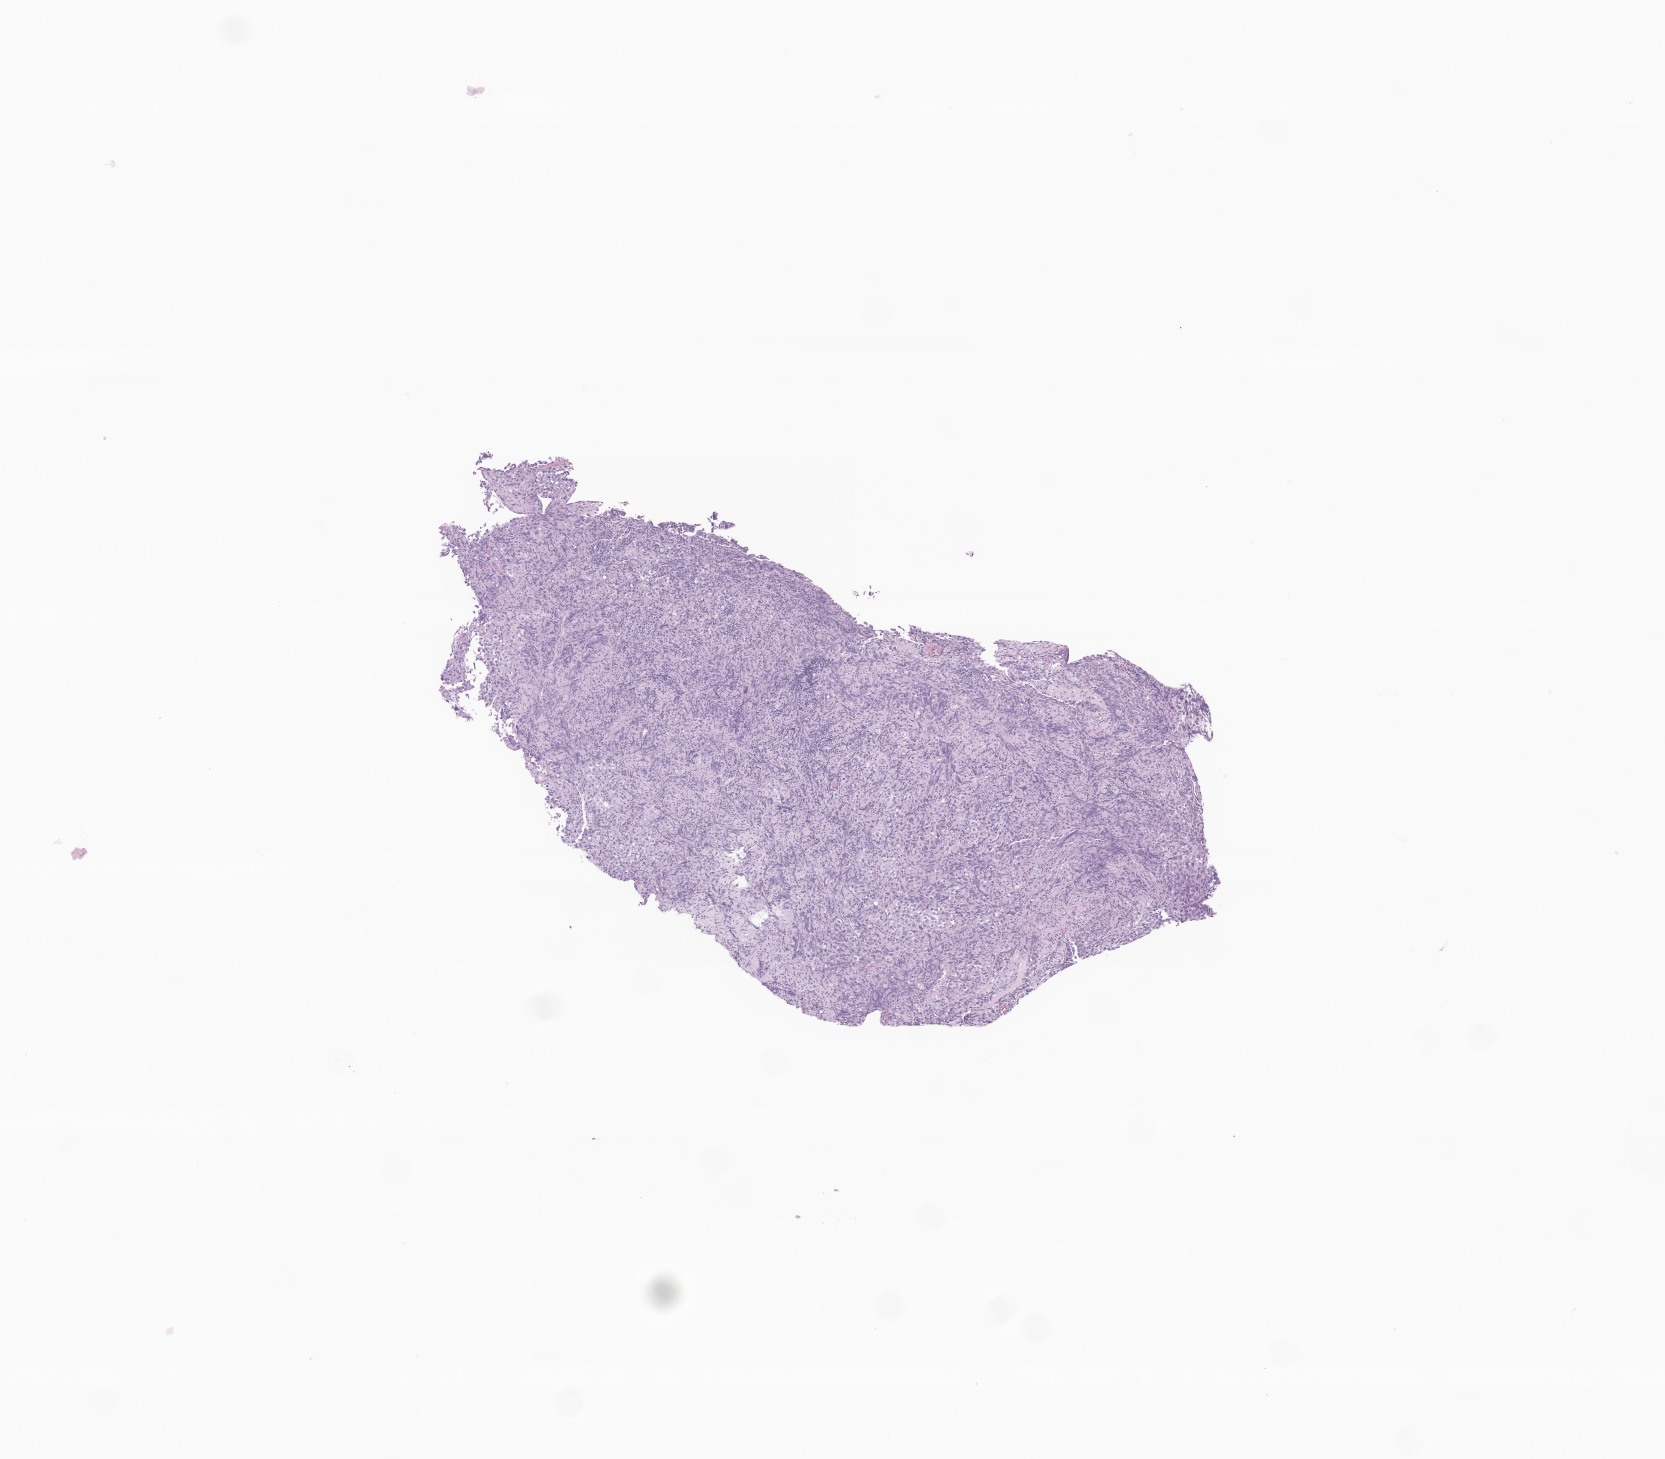
Whole-slide image, haematoxylin and eosin stain of tumor tissue from the brain, shown as a low-resolution overview of the whole scanned area (about 7.0 x 6.2 mm). FFPE section. Patient male; age 208 months (17 years 4 months).
Diagnosis (ICD-O-3 morphology term): Germinoma.